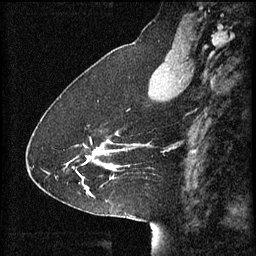
Breast MRI (dynamic contrast-enhanced), one sagittal slice. Position 22 of 60 along the scan axis. 3 images stored at this slice position (order not interpretable as contrast timing). 1.5 T. TE 4.2 ms, TR 8.2 ms. 2 mm slice thickness. 256 × 256 image matrix, field of view 200 × 200 mm. Patient: female, 41 years.
Annotated regions visible in this slice (semi-automatic segmentation, software-assisted and operator-edited):
- analysis volume of interest (the breast-tissue region the enhancement analysis was run in; not a lesion): bounding box (x1, y1, x2, y2) in pixels: (66, 132, 128, 181)
- tumour enhancement mask (voxels above the 70 % enhancement threshold inside the analysis volume of interest): (68, 134, 125, 179)